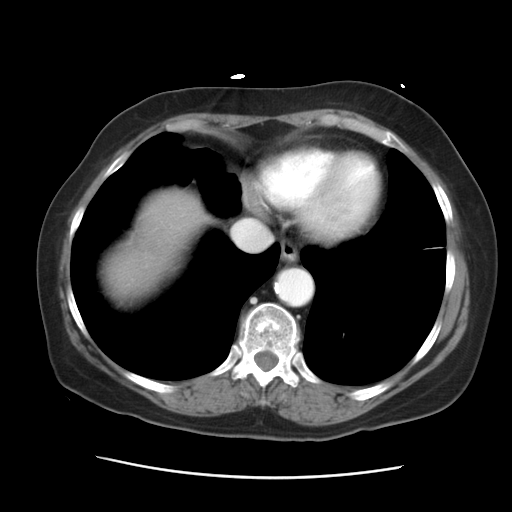
Contrast-enhanced abdominal CT, one axial slice; position 26 of 29 along the scan axis; reconstruction kernel STANDARD; 120 kVp; soft-tissue window (W 400 / L 40 HU); 7.5 mm slice thickness; 512 × 512 image matrix, field of view 354 × 354 mm. Female patient, age 64 years. Case-level facts recorded for this patient, not image findings: diagnosis: colorectal cancer liver metastases, imaged before liver resection.
Structures marked on this image (outlined manually by an expert reader):
- hepatic veins: bounding box <232,220,268,250> (left, top, right, bottom; pixels)
- liver: <101,190,206,300>
- planned liver remnant (the part of the liver to remain after resection): <109,192,202,261>